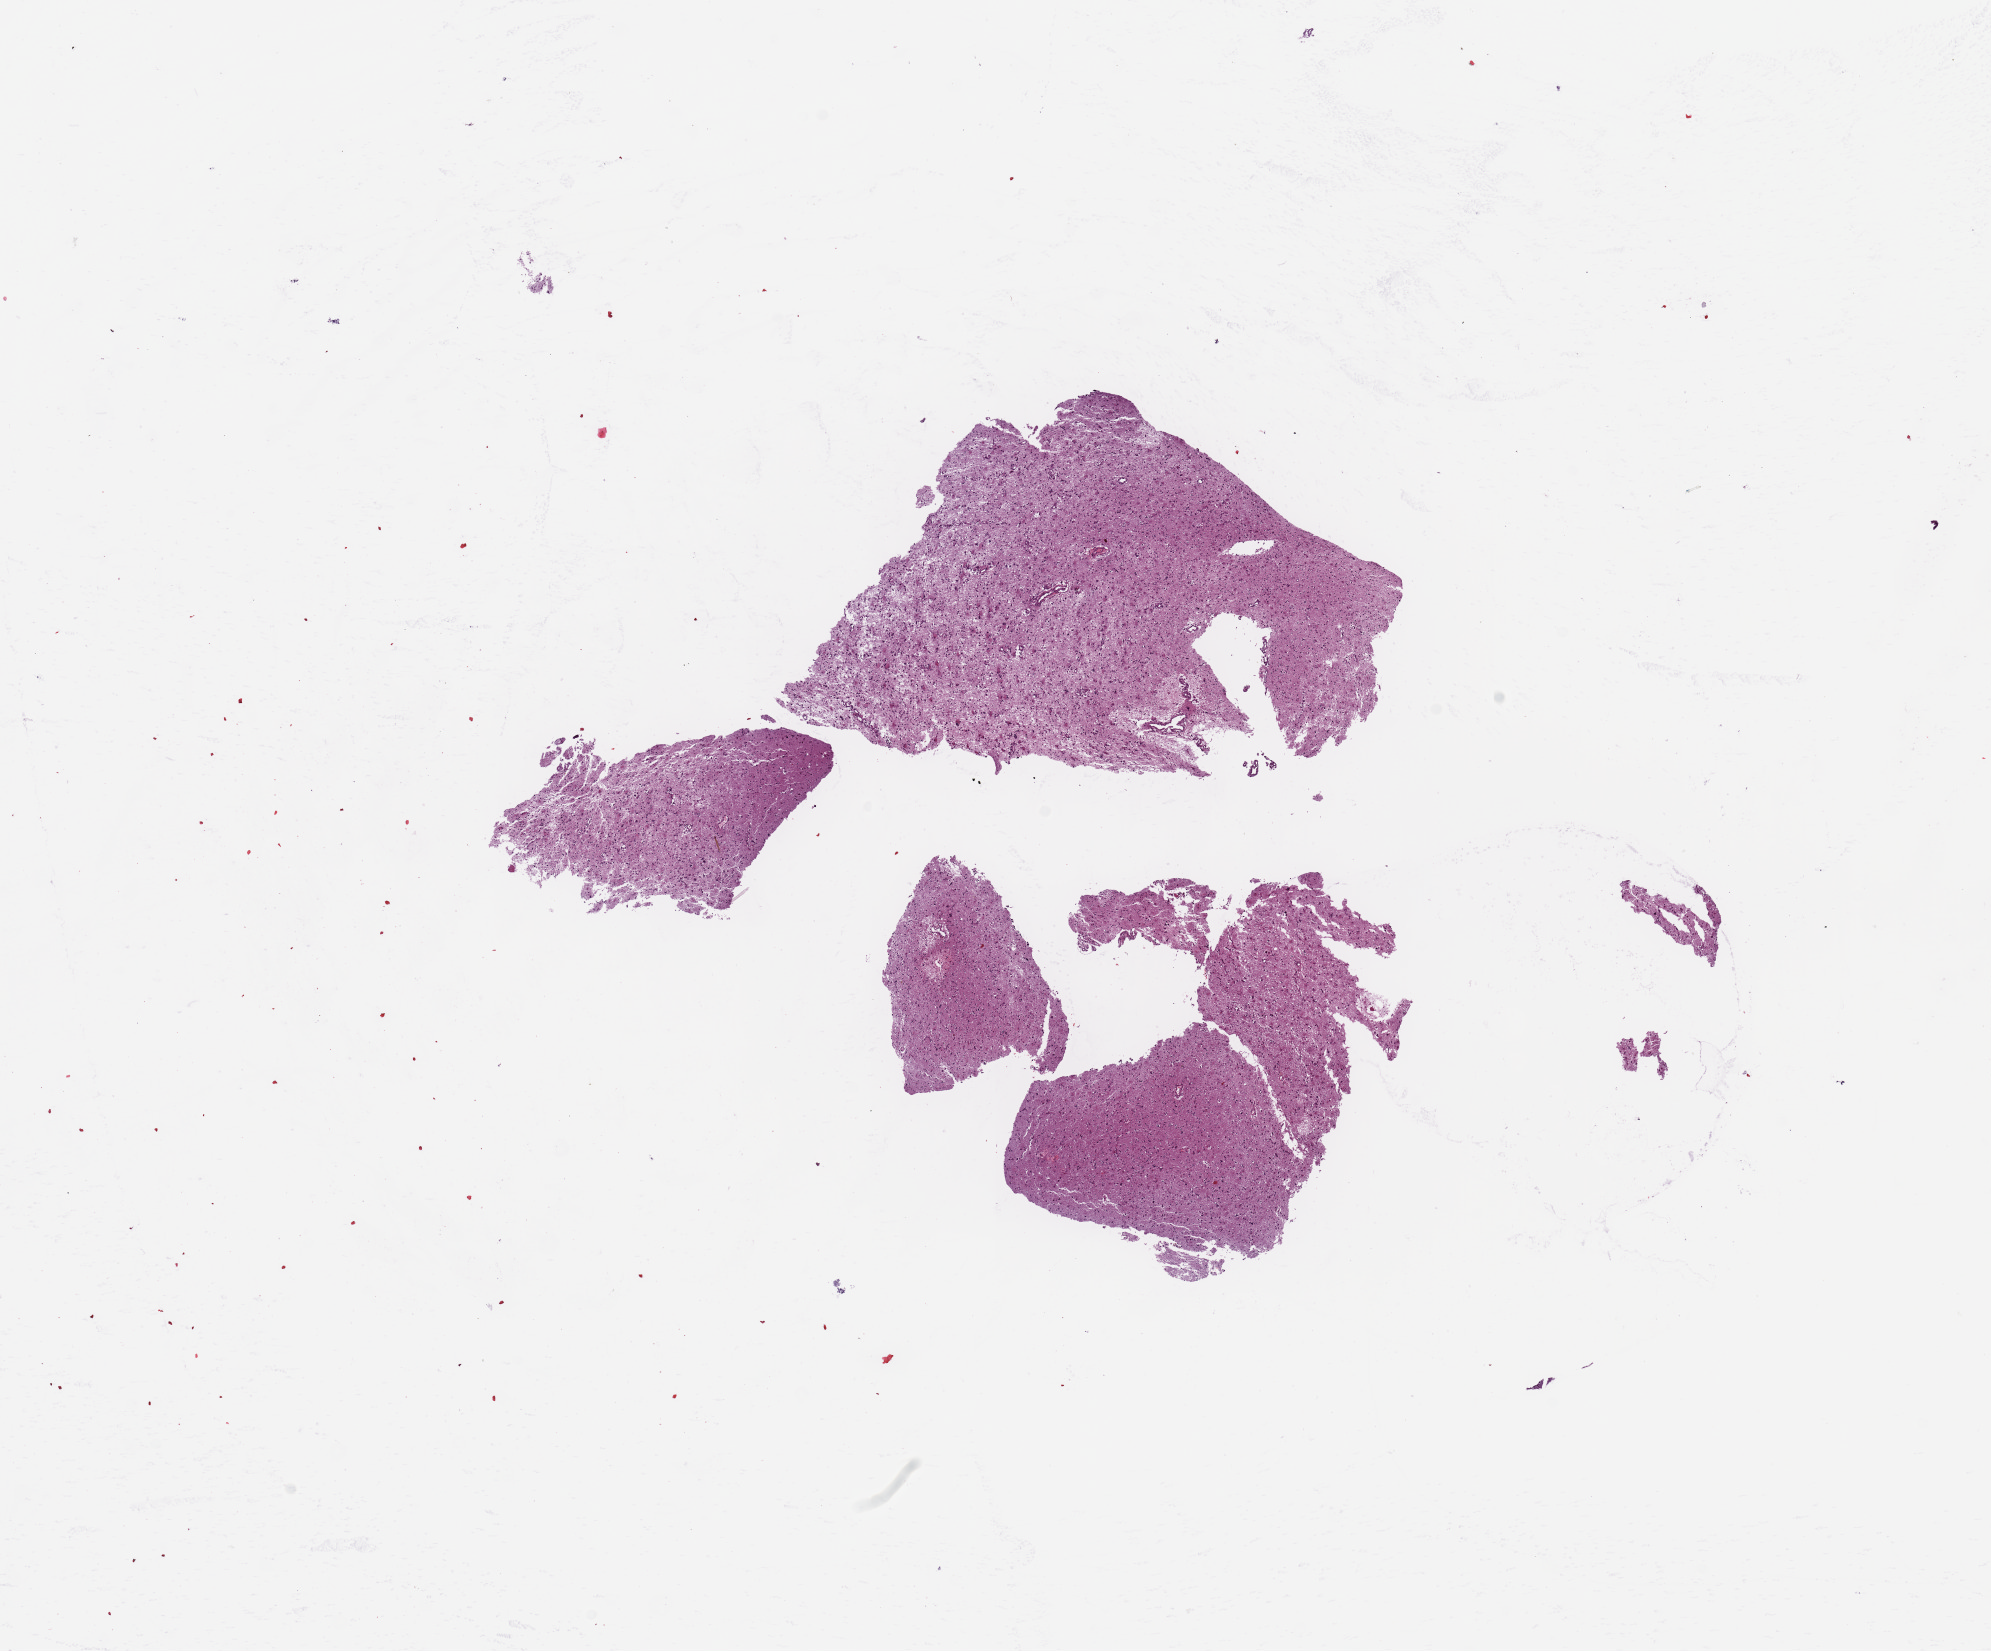
H&E whole-slide image — shown as a low-resolution overview of the whole scanned area (about 15.8 x 13.1 mm, acquisition: 20x scan). Brain, tumour tissue. Patient: male, age 43 years.
- patient diagnosis (cohort enrolment): glioblastoma multiforme (brain)